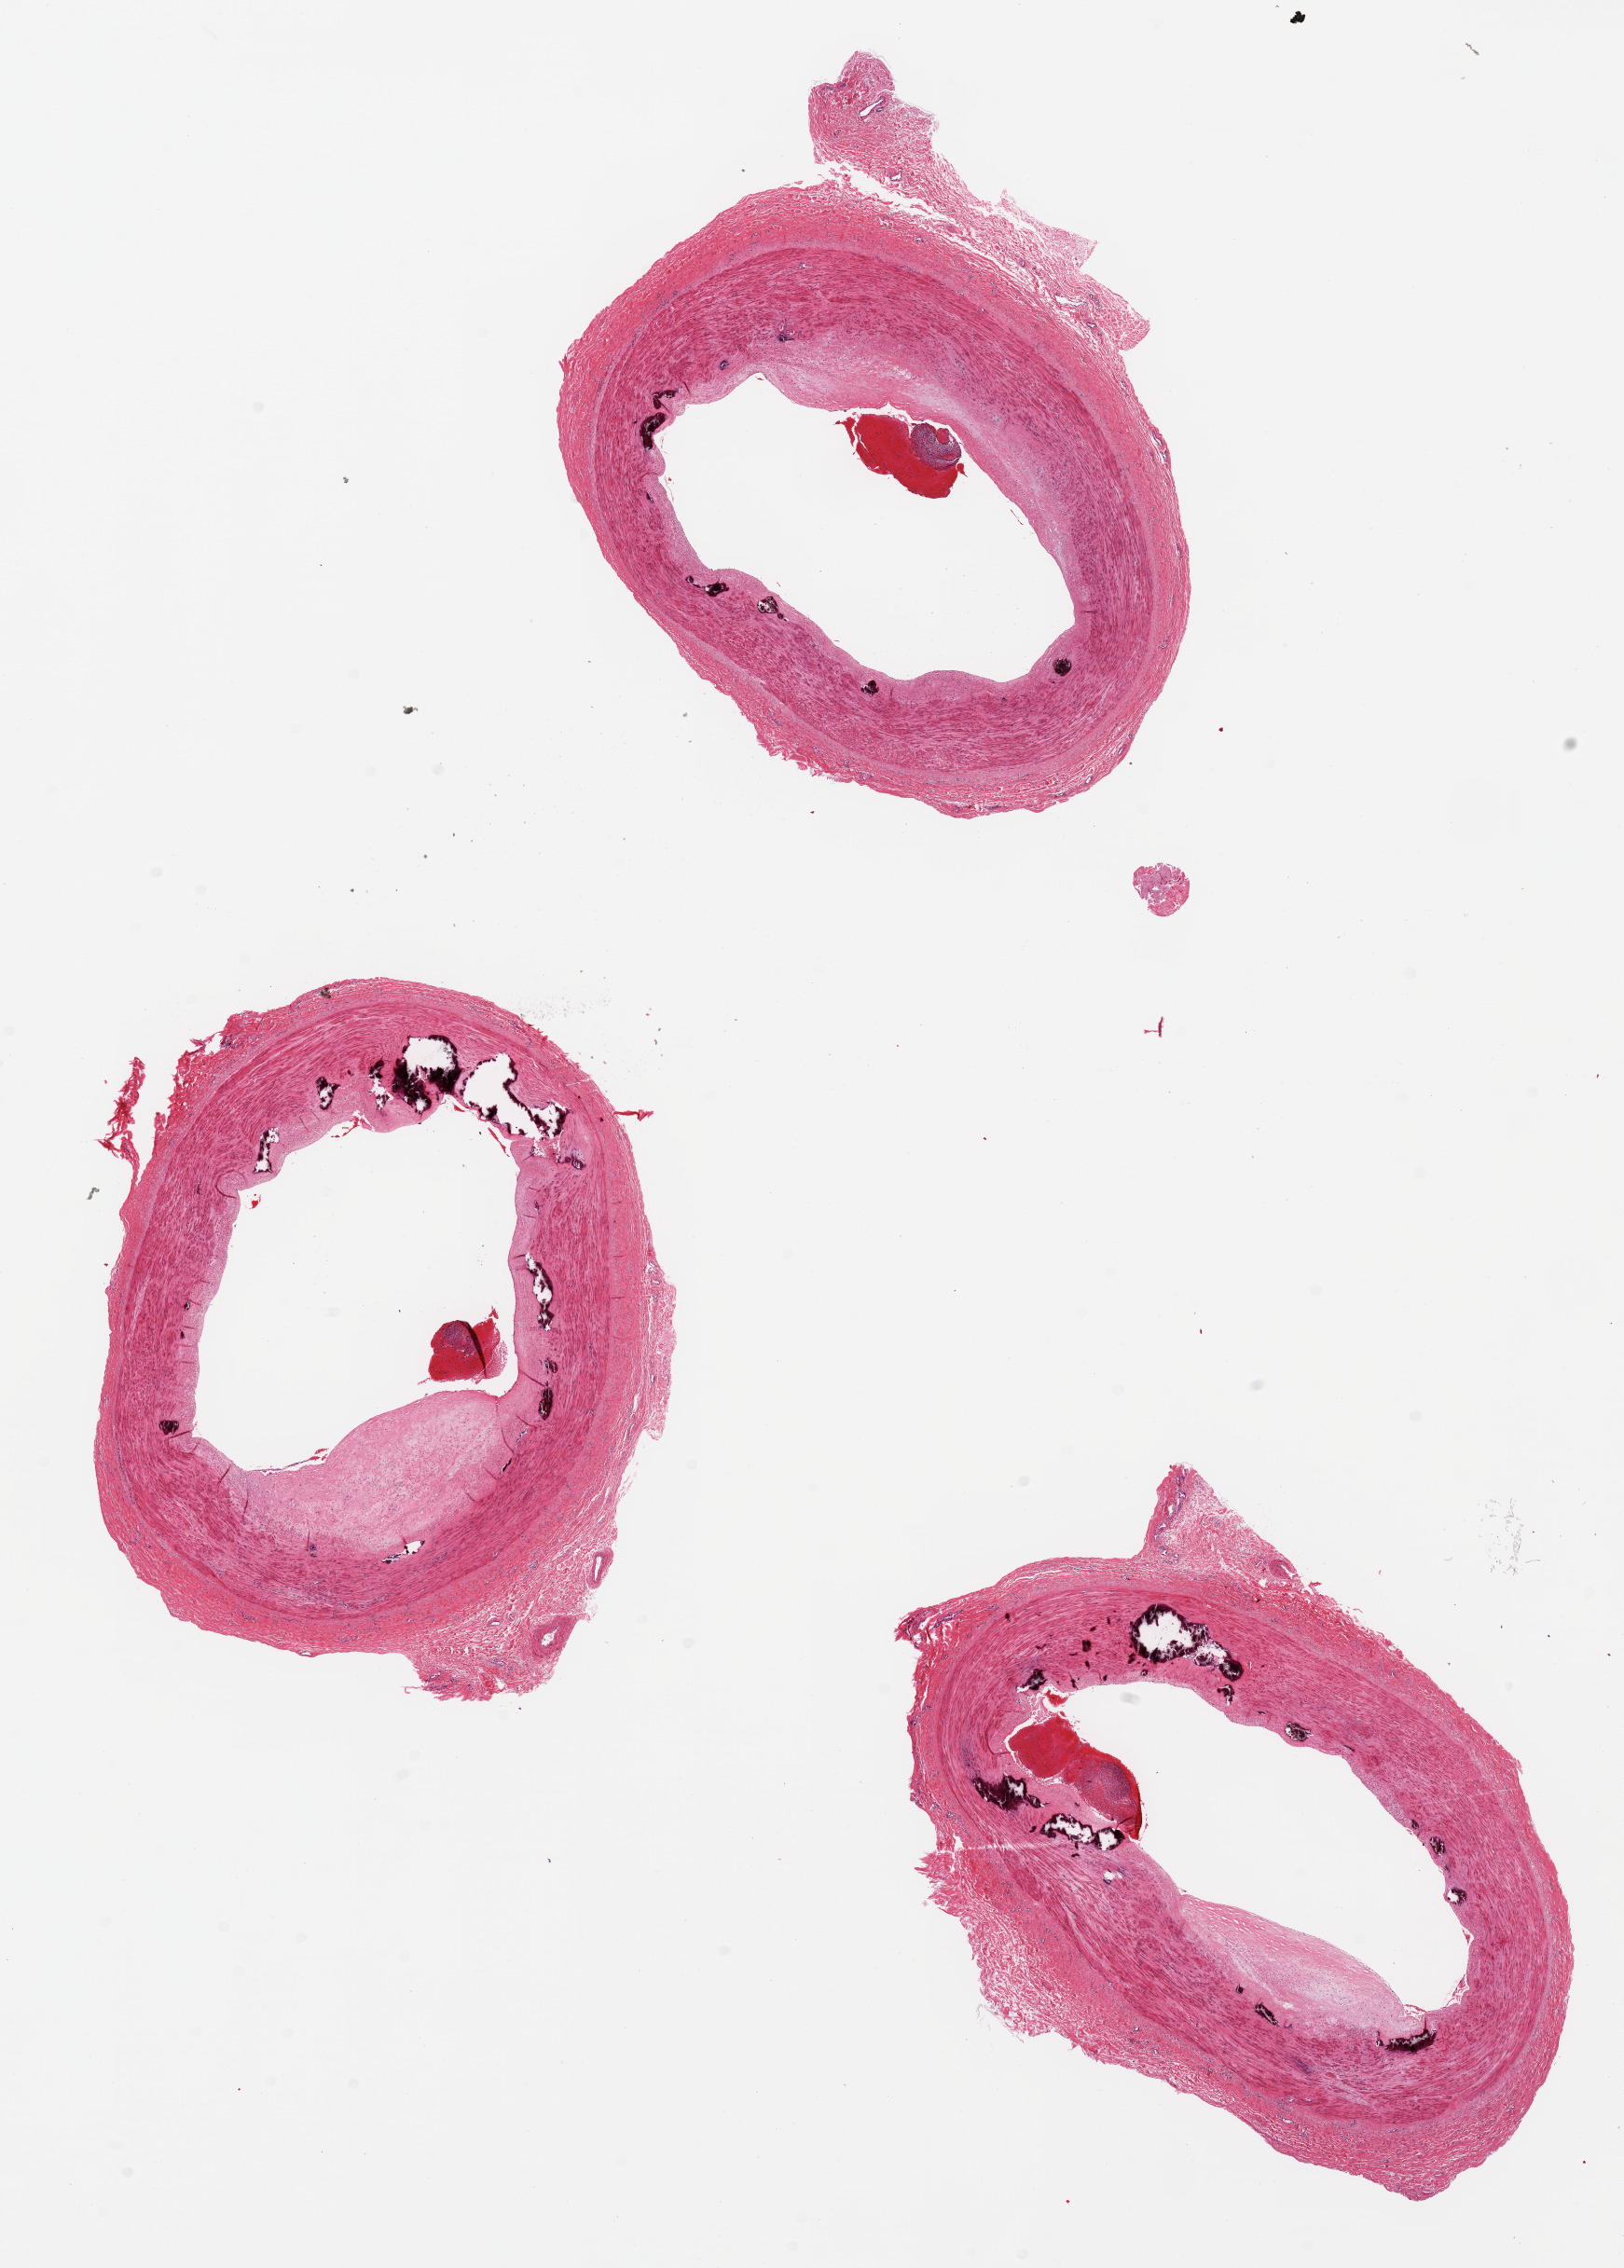
H&E whole-slide image, brightfield, low-resolution overview of the scanned area, about 13.8 x 19.2 mm; PAXgene-fixed paraffin-embedded (PFPE) section; sampled site (target tissue): tibial artery; tissue donor sample. Donor: male.
Reviewer comment on this tissue sample: 3 pieces; moderate intimal atherosclerosis; intimal and medial calcifications; well trimmed.